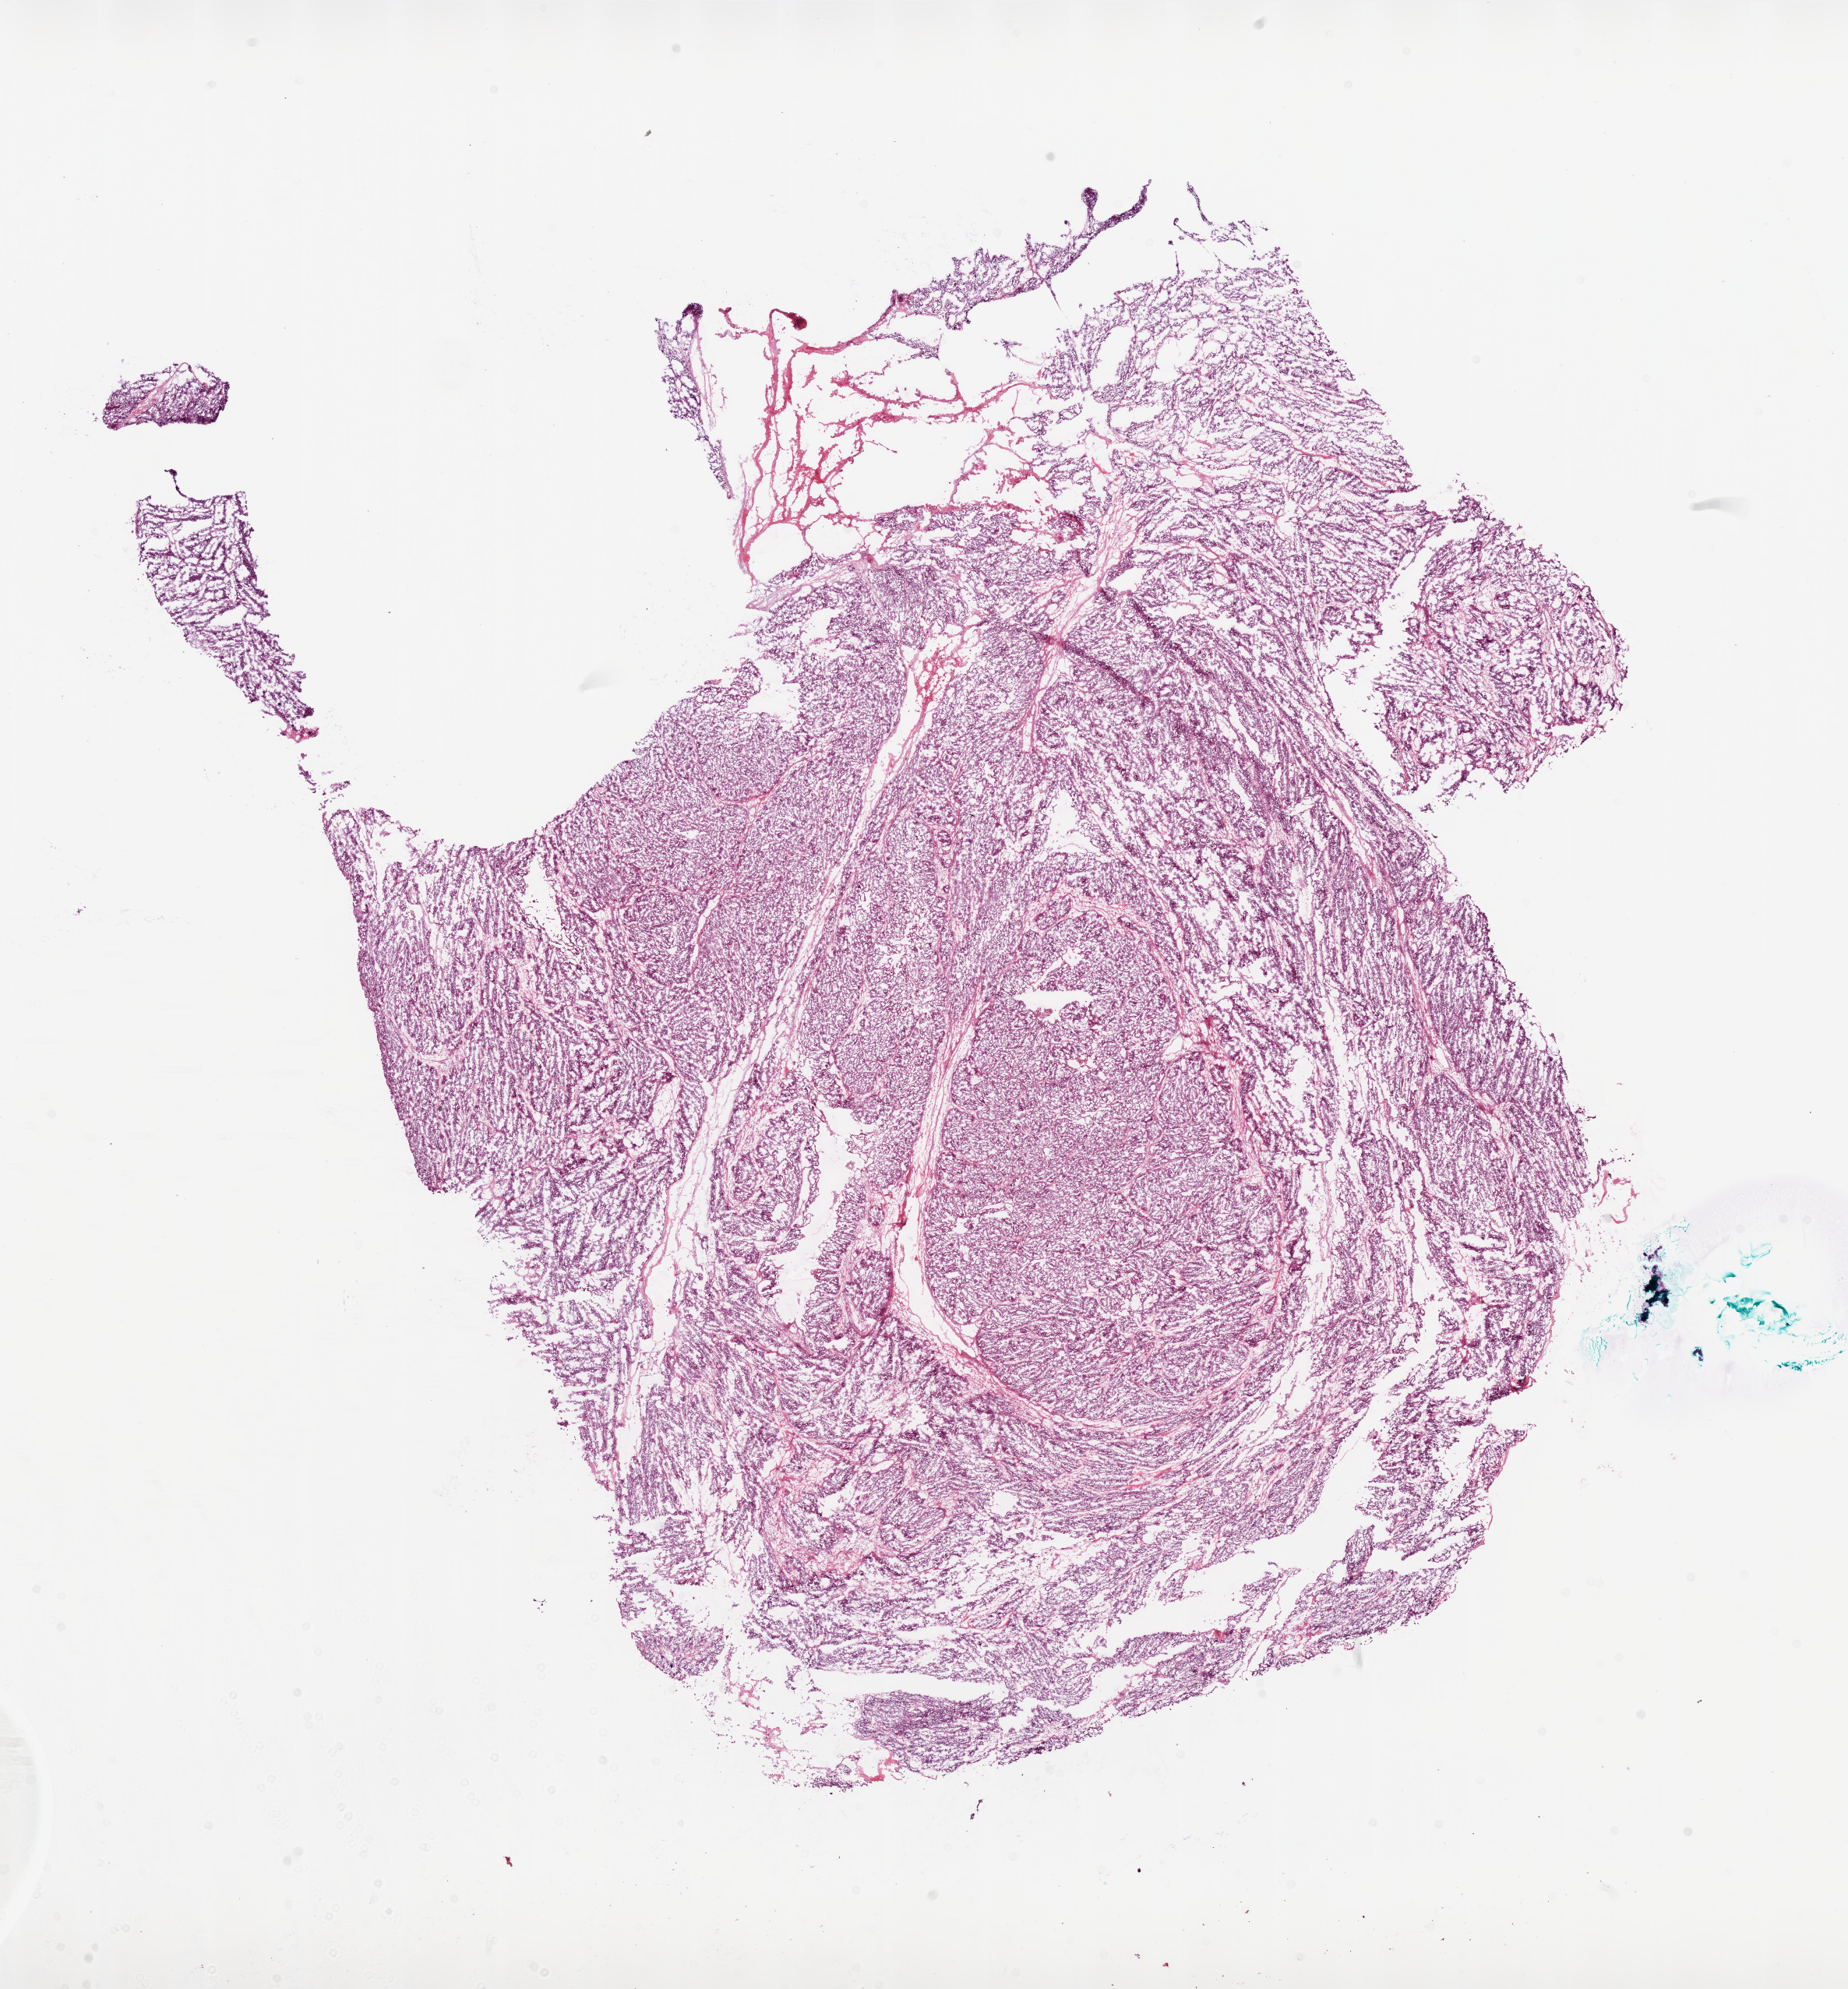
H&E whole-slide image, whole scanned area (about 19.0 x 20.4 mm, from a 20x scan) shown as a low-resolution overview. Frozen section from the bottom of the tissue portion. Ovary, primary tumour sample. Female, age 72 years at initial diagnosis. Histologic grade: G3 (poorly differentiated). Slide review estimates, as recorded: tumour cells 85%, tumour nuclei 90%, normal cells 0%, stromal cells 15%, necrosis 0%.
FIGO stage: IIIC. Laterality: bilateral. Pathologic diagnosis: Serous cystadenocarcinoma, NOS.